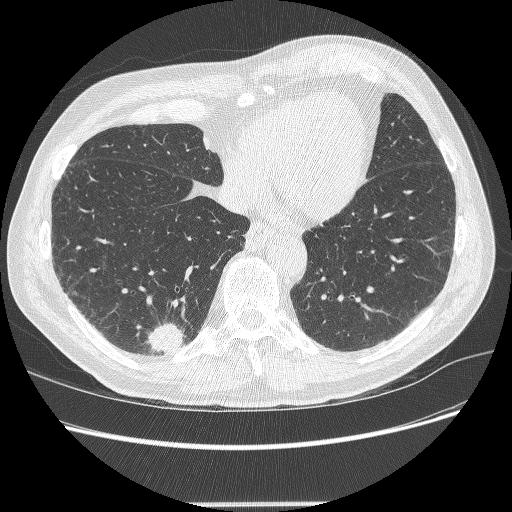
Axial slice from a low-dose chest CT screening exam; second screening round (one year after baseline); lung window (W 1500 / L -600 HU); lung (sharp) reconstruction kernel (BONE); 512 × 512 image matrix. Male, age 71 years at enrolment. Current smoker at enrolment.
Expert-annotated lung lesion, bounding box <137,322,188,362> (left, top, right, bottom; pixels). The screening reader recorded 5 non-calcified nodules or masses ≥4 mm on this exam (right lower lobe, right lower lobe, right upper lobe, right upper lobe, right upper lobe); which of them this box marks is not recorded. Lung cancer was diagnosed 7 days after this screen: squamous cell carcinoma, NOS, right lower lobe, moderately differentiated (G2), stage IA (AJCC 6th edition), 27 mm at pathology.